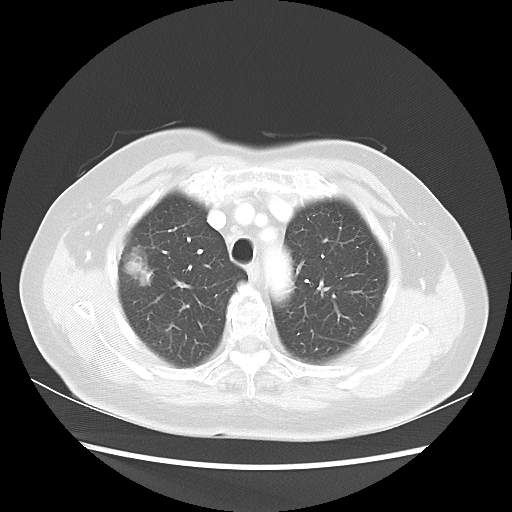
Chest CT, one axial slice; 100 kVp; lung window (W 1500 / L -600 HU); 5 mm slice thickness; 512 × 512 image matrix, field of view 360 × 360 mm. Female patient, age 75 years. Case-level facts recorded for this patient, not image findings: clinical TNM (as recorded): T1c N0 M0.
Outlined on this slice (bounding box drawn by a radiologist):
- lung tumour (recorded histology: adenocarcinoma): bounding box <122,243,153,289> (left, top, right, bottom; pixels)